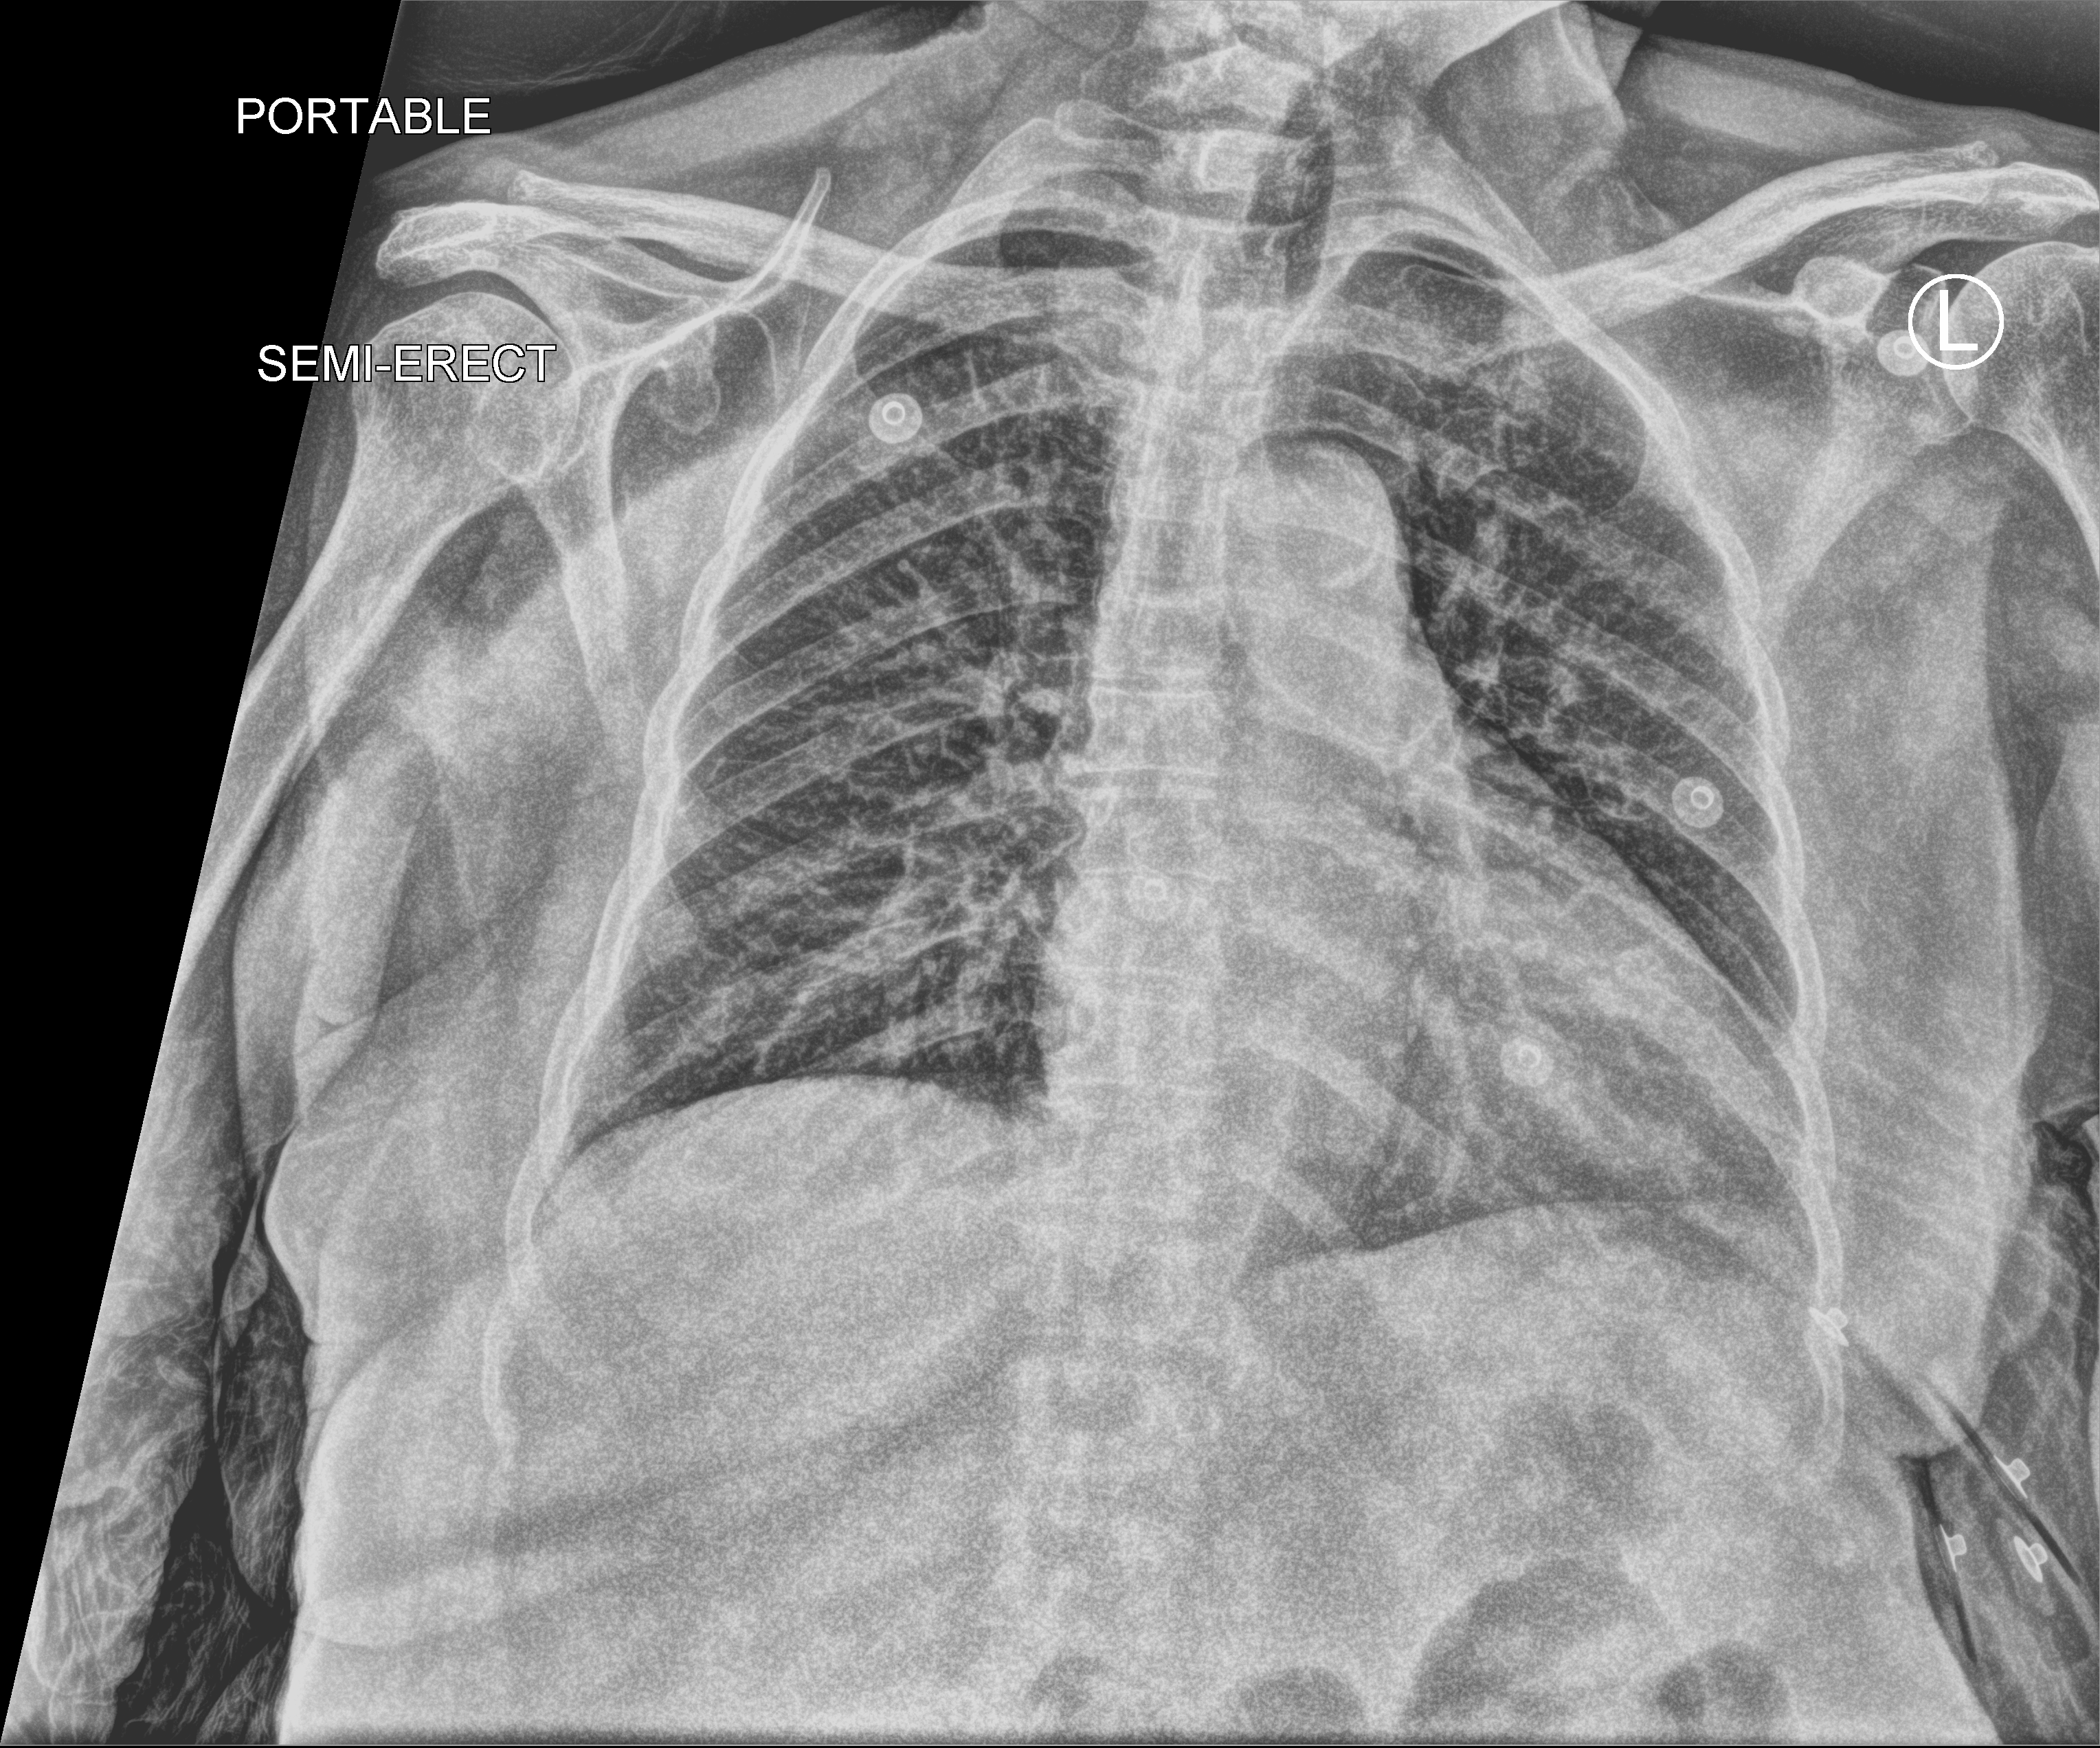
Portable chest radiograph, anteroposterior (AP) projection. Female patient hospitalised with COVID-19, age 75–90 years.
Hospital-stay facts (about this admission, not read from this image; timing relative to this image not recorded): mechanically ventilated during this hospital stay: no.